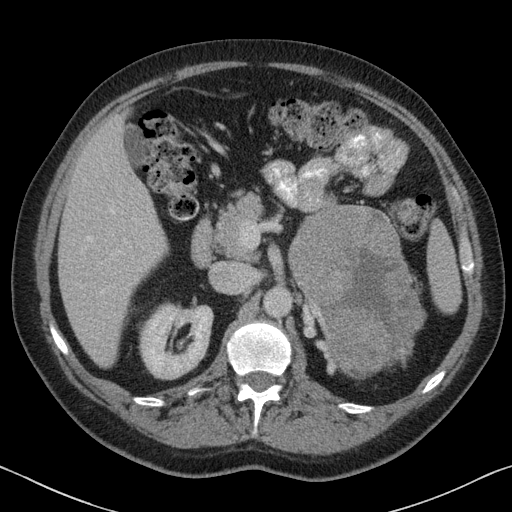
Contrast-enhanced abdominal CT, one axial slice; position 45 of 88 along the scan axis; soft-tissue window (W 400 / L 40 HU); 3 mm slice thickness; 512 × 512 image matrix, field of view 366 × 366 mm. Patient: male, 51 years. Case-level facts recorded for this patient, not image findings: diagnosis: adrenocortical carcinoma; tumour side: left adrenal; tumour size at pathology: 16.5 cm; Ki-67 index: 30 %; stage (as recorded): 2.
Structures marked on this image (semi-automatic segmentation, software-assisted and operator-edited):
- mass: bounding box [x1, y1, x2, y2] px = [289, 207, 423, 376]